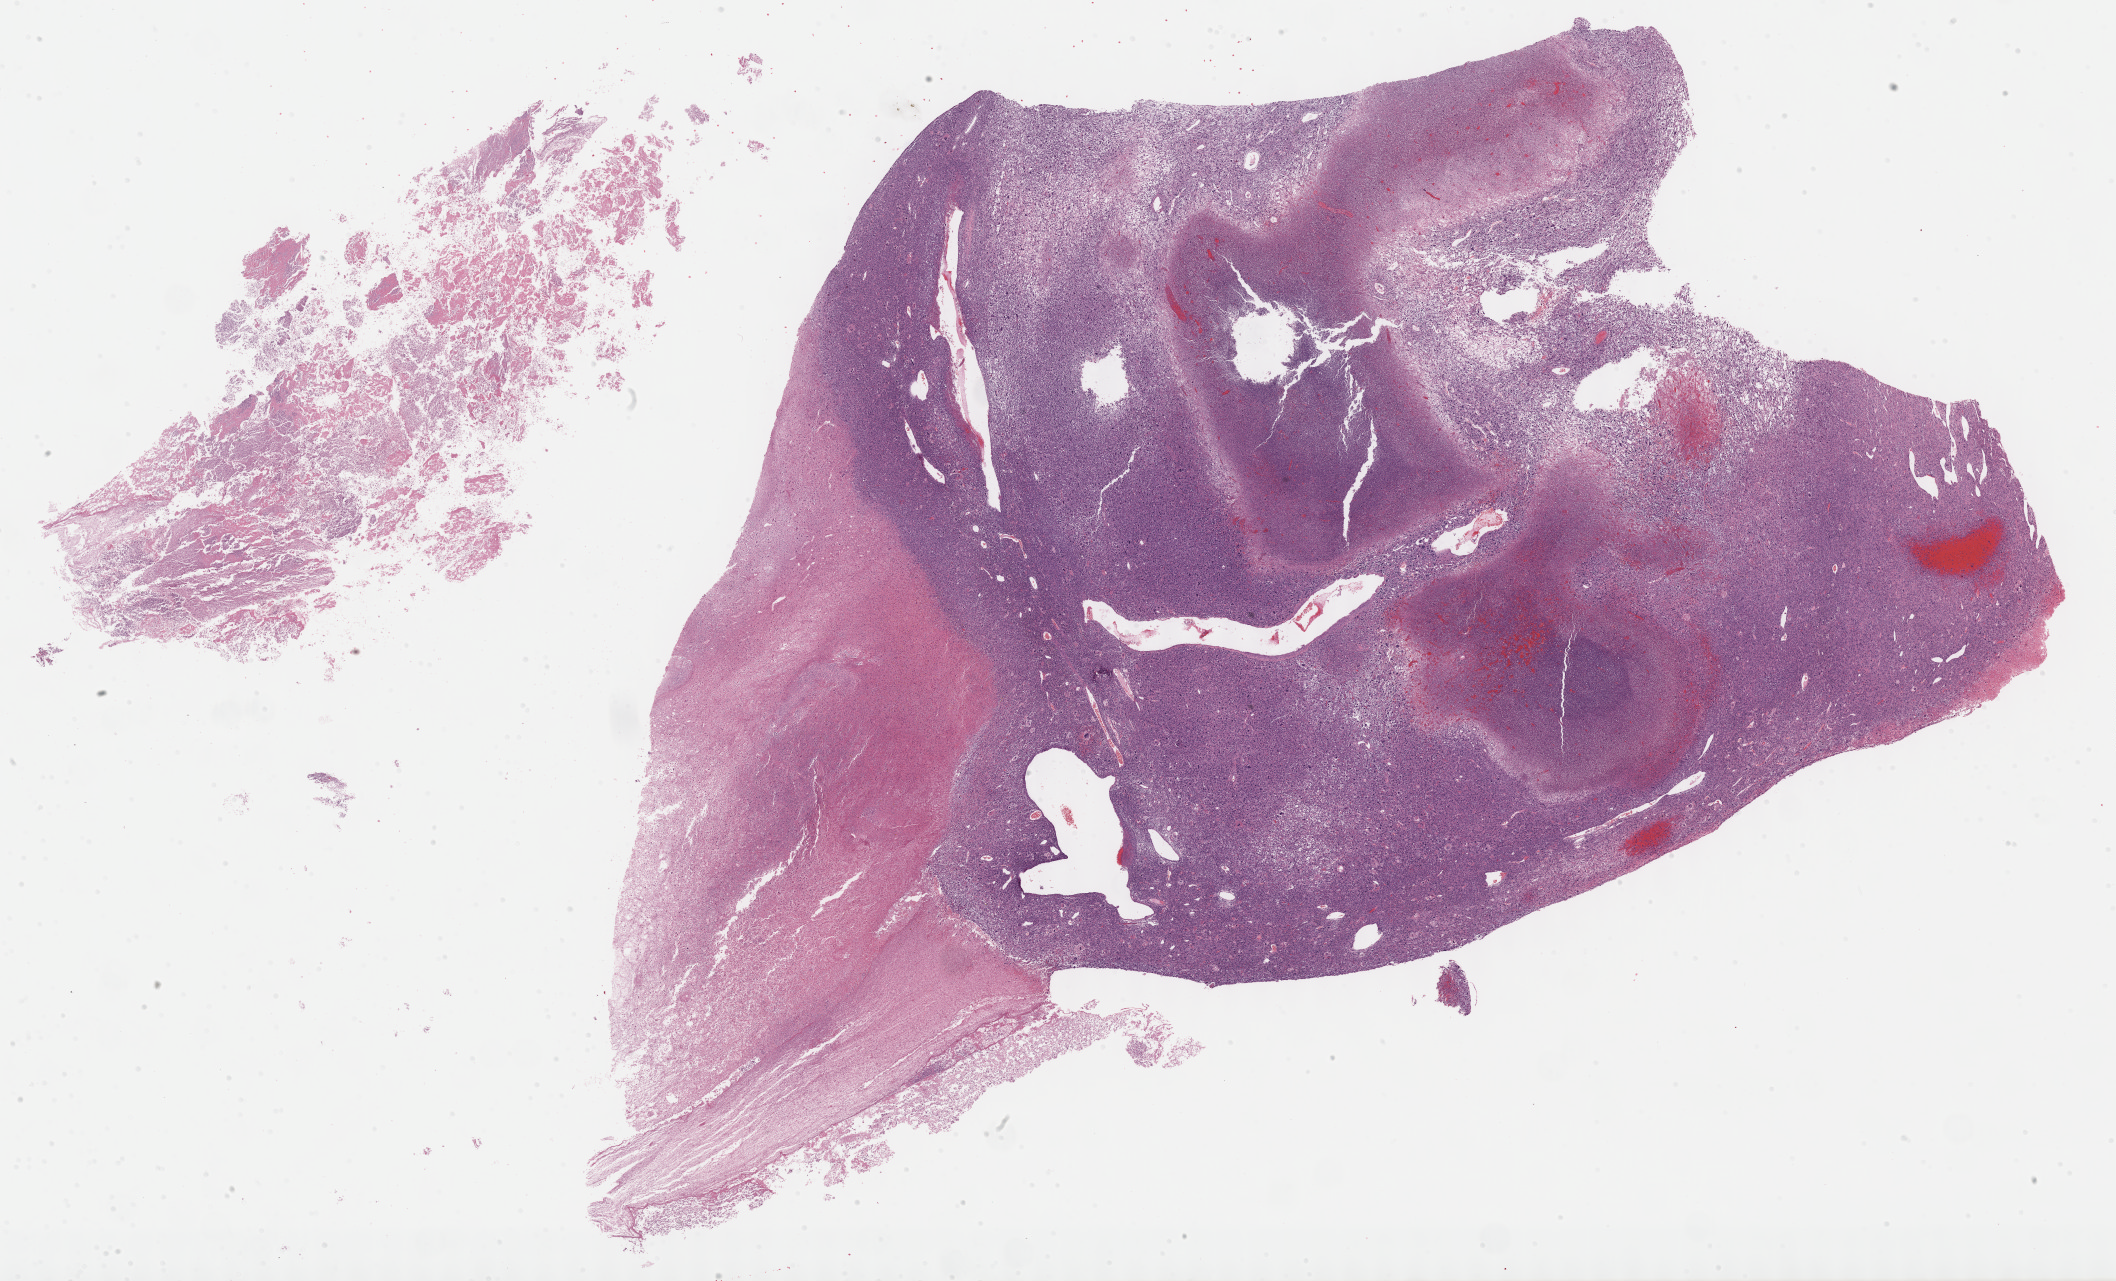
Hematoxylin and eosin (H&E) stained whole-slide image, shown as a low-resolution overview of the whole scanned area (about 34.2 x 20.7 mm, acquisition: 40x scan), formalin-fixed paraffin-embedded (FFPE) diagnostic section, sample: primary tumour, connective, subcutaneous and other soft tissues. Patient: male, age at initial diagnosis 79 years.
Pathologic diagnosis: Malignant fibrous histiocytoma.